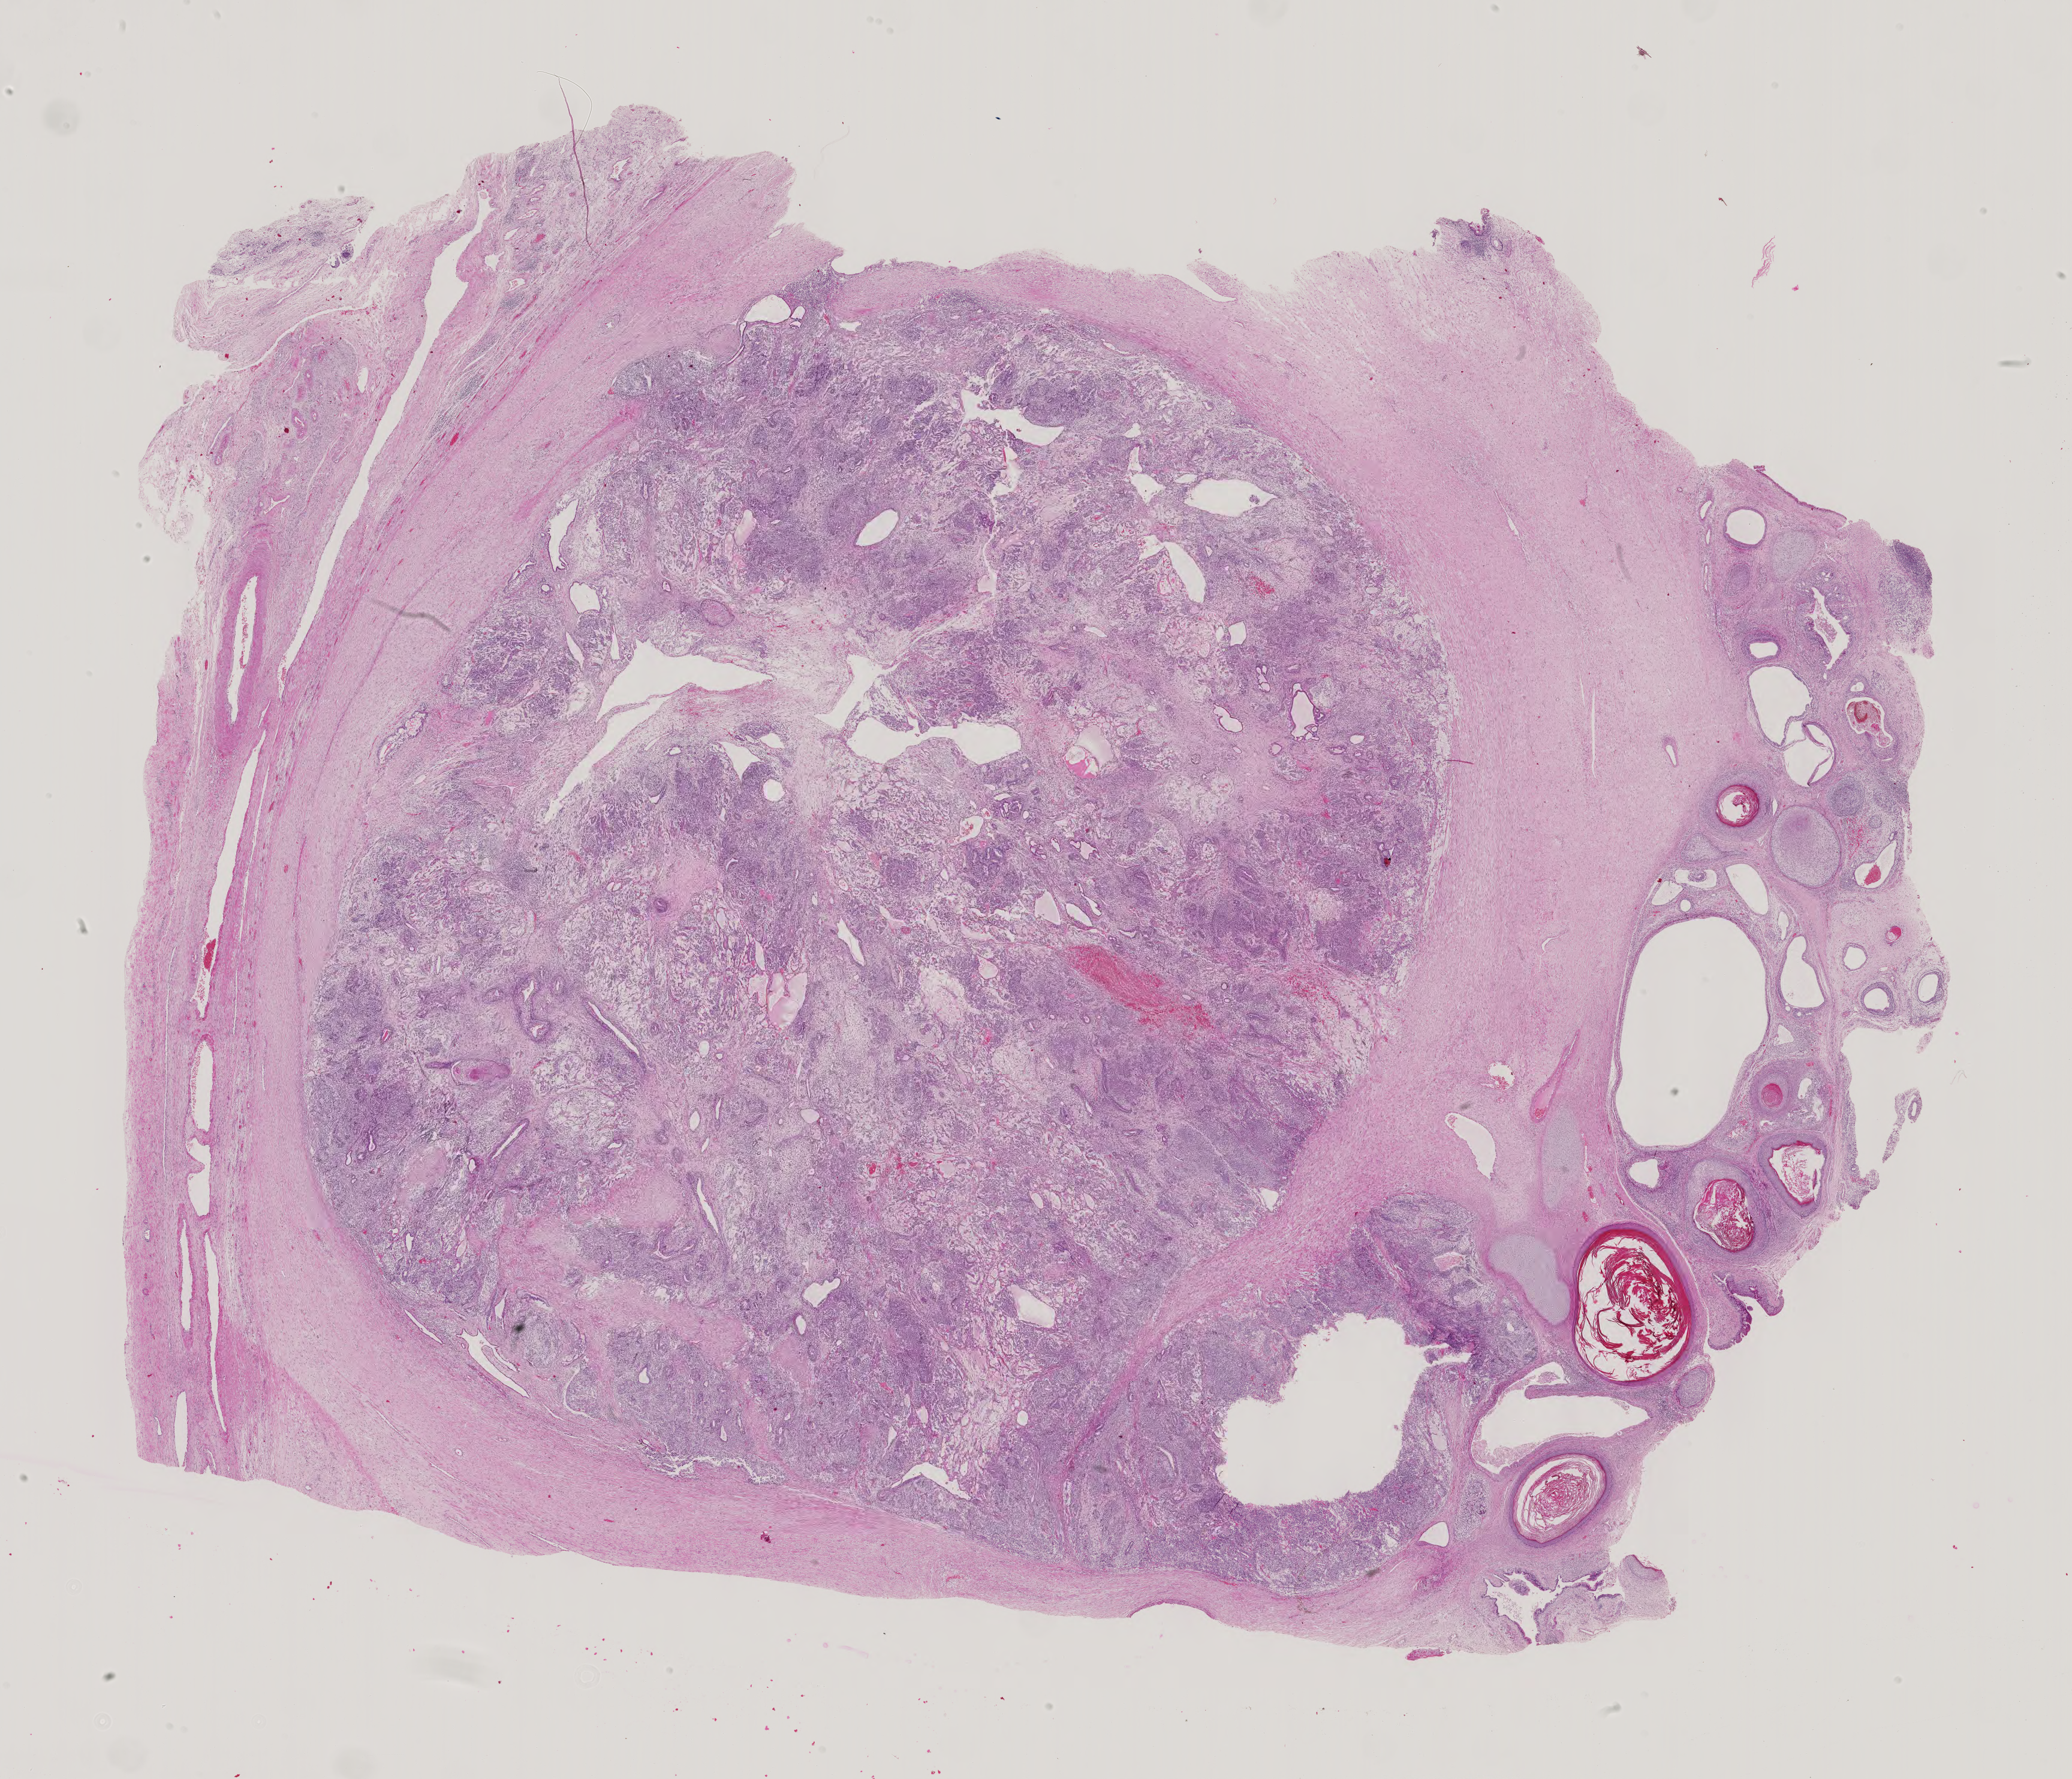
H&E whole-slide image — whole scanned area (about 25.2 x 21.6 mm, acquisition: 40x scan) shown as a low-resolution overview. Male patient.
* specimen: formalin-fixed paraffin-embedded (FFPE) diagnostic section; primary tumour sample from the testis